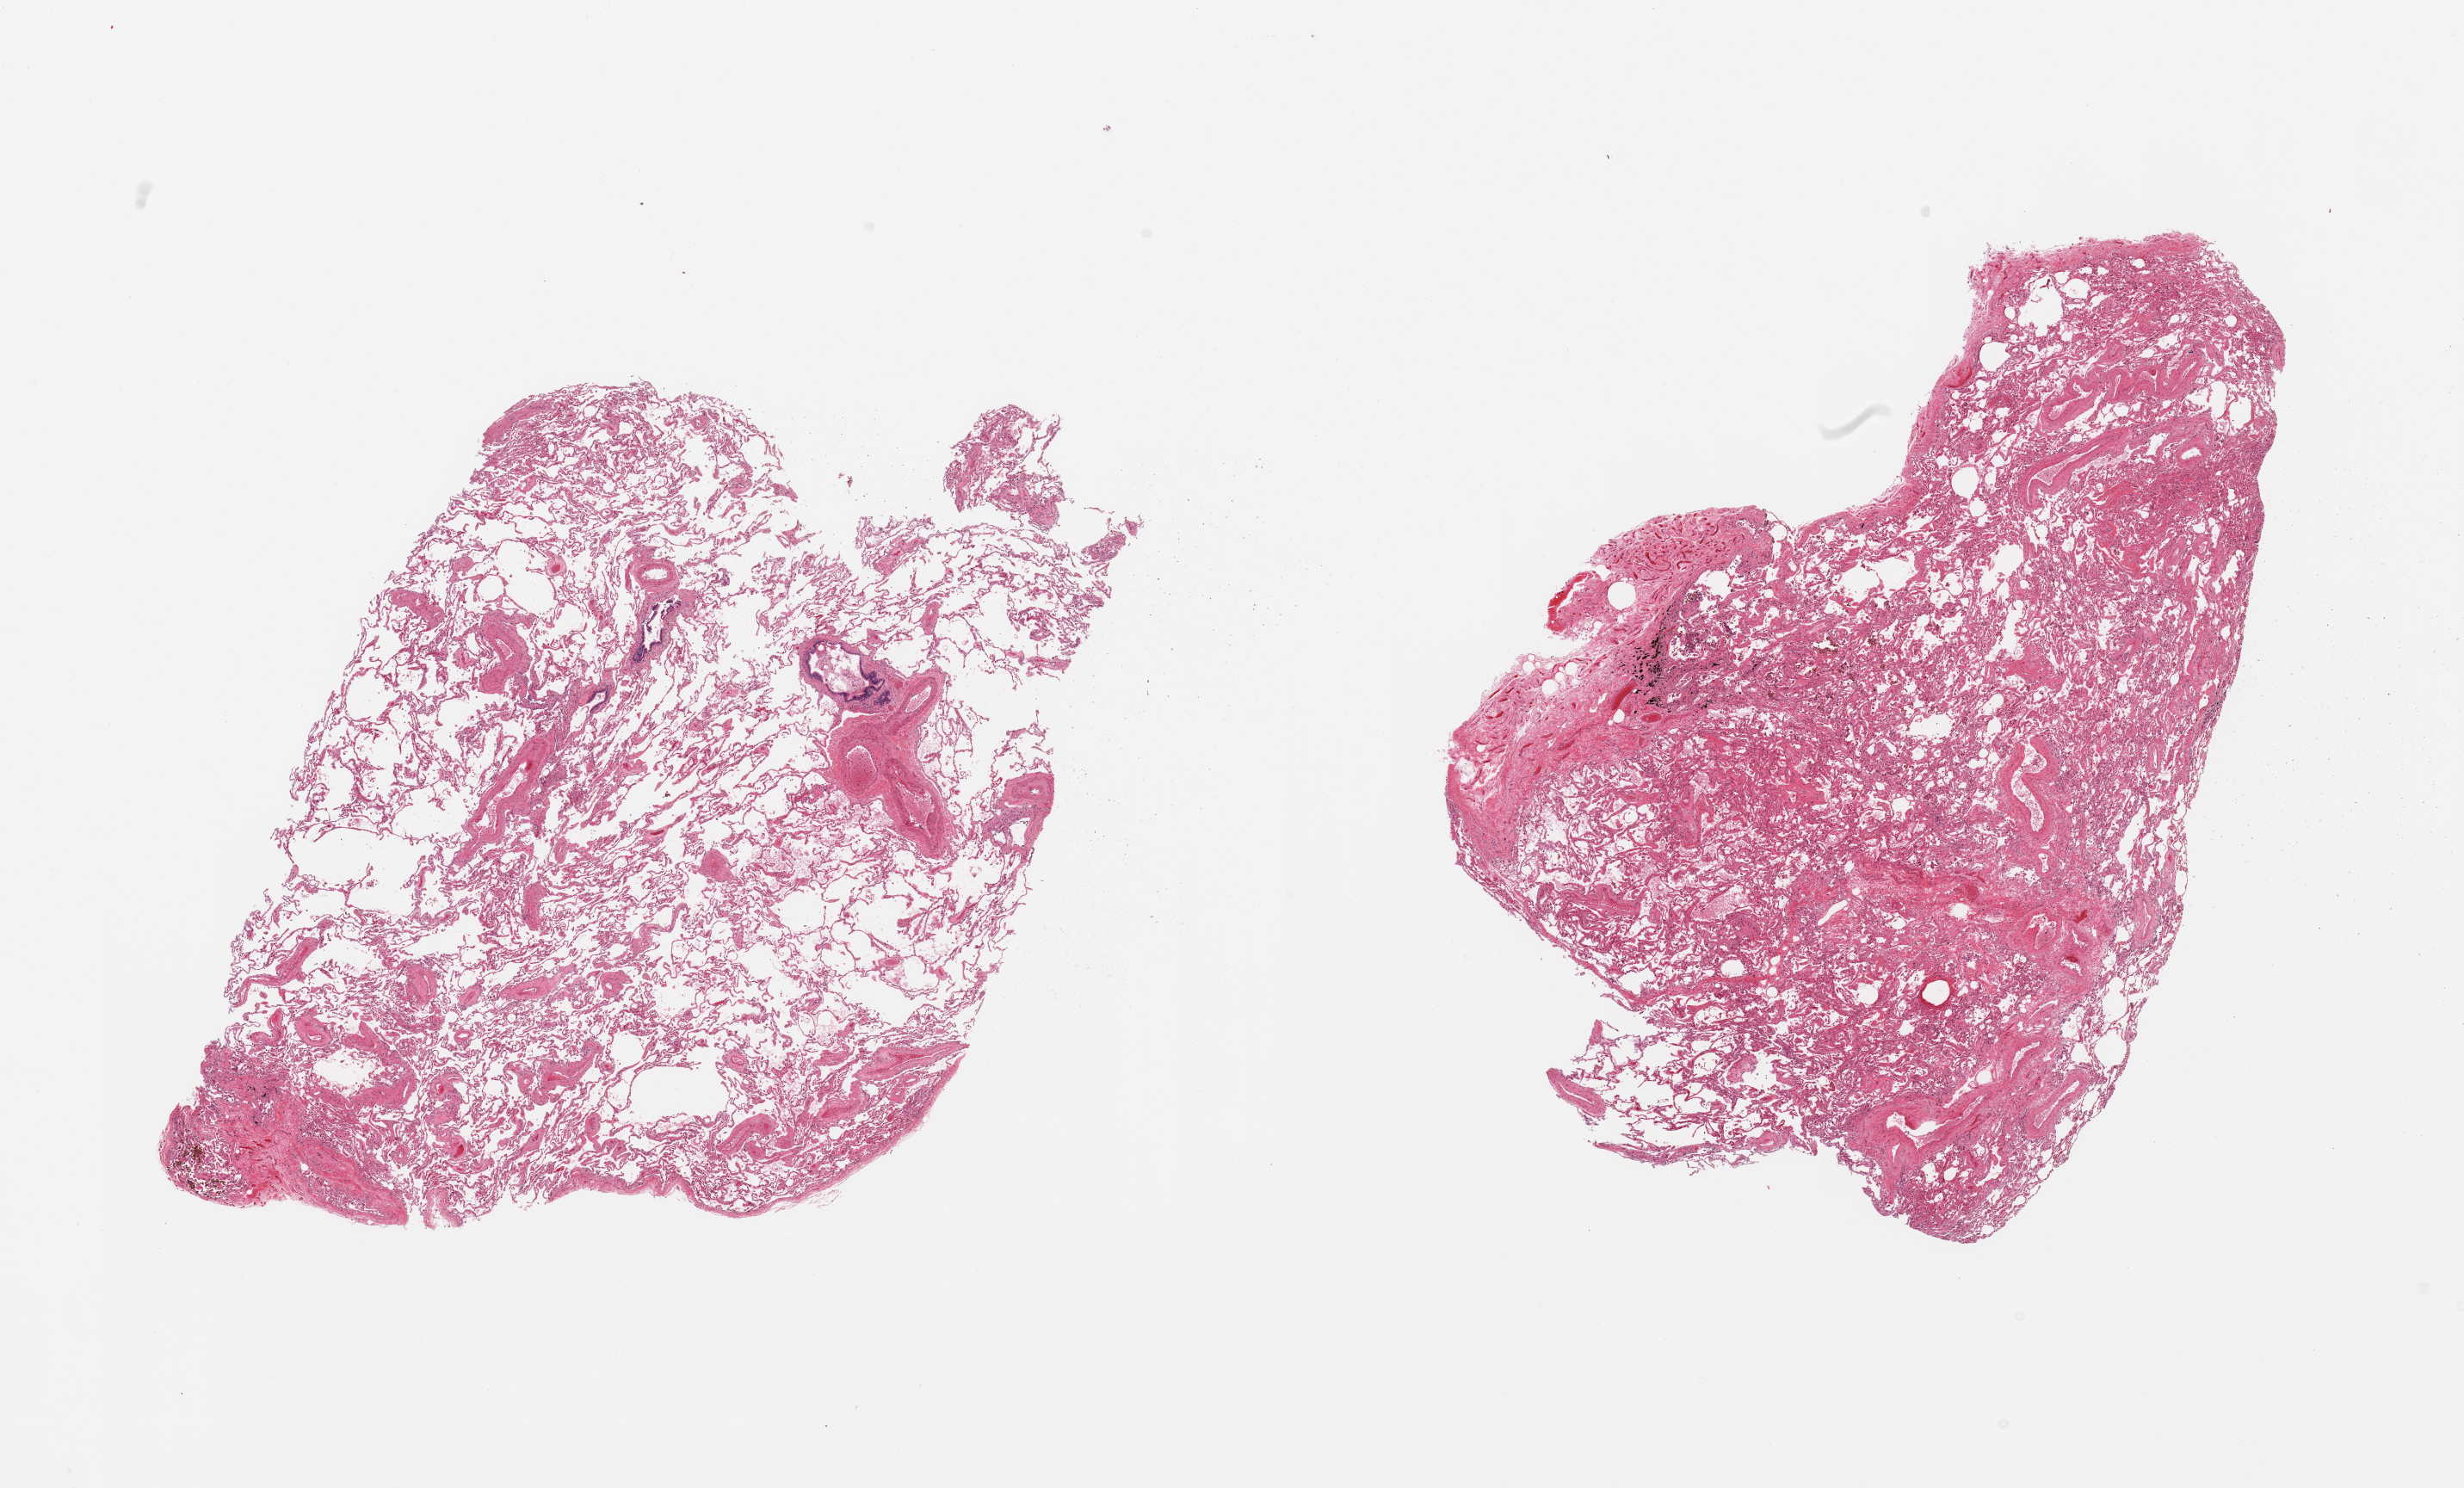
Digitized haematoxylin and eosin-stained section, brightfield — low-resolution overview of the scanned area, about 22.6 x 13.7 mm, PAXgene-fixed, paraffin-embedded tissue, section of lung (target tissue), tissue donor sample. Donor sex: male.
- review note (as recorded): 2 pieces, patchy mild/moderate congestion/edema